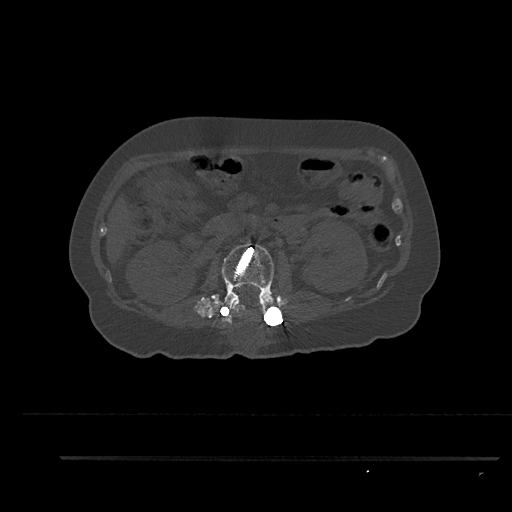
CT including the spine, one axial slice; reconstruction kernel Br40s/3; 120 kVp; bone window (W 1800 / L 400 HU); 0.5 mm slice thickness; 512 × 512 image matrix, field of view 408 × 408 mm. Patient: female, 44 years. Case-level facts recorded for this patient, not image findings: primary cancer: renal.
Structures marked on this image (semi-automatically segmented with operator editing):
- L2 vertebra: box from (x=215, y=242) to (x=275, y=321) px